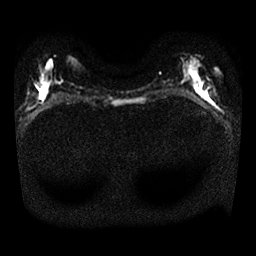
Breast MRI, one axial slice; position 10 of 25 along the scan axis; diffusion-weighted series; image 2 of 4 stored at this slice position (different b-values; order by instance number); 1.5 T; 256 × 256 image matrix. Female patient.
Outlined on this slice (outlined manually by an expert reader):
- tumour on diffusion-weighted imaging: bounding box [x1, y1, x2, y2] px = [205, 95, 210, 101]